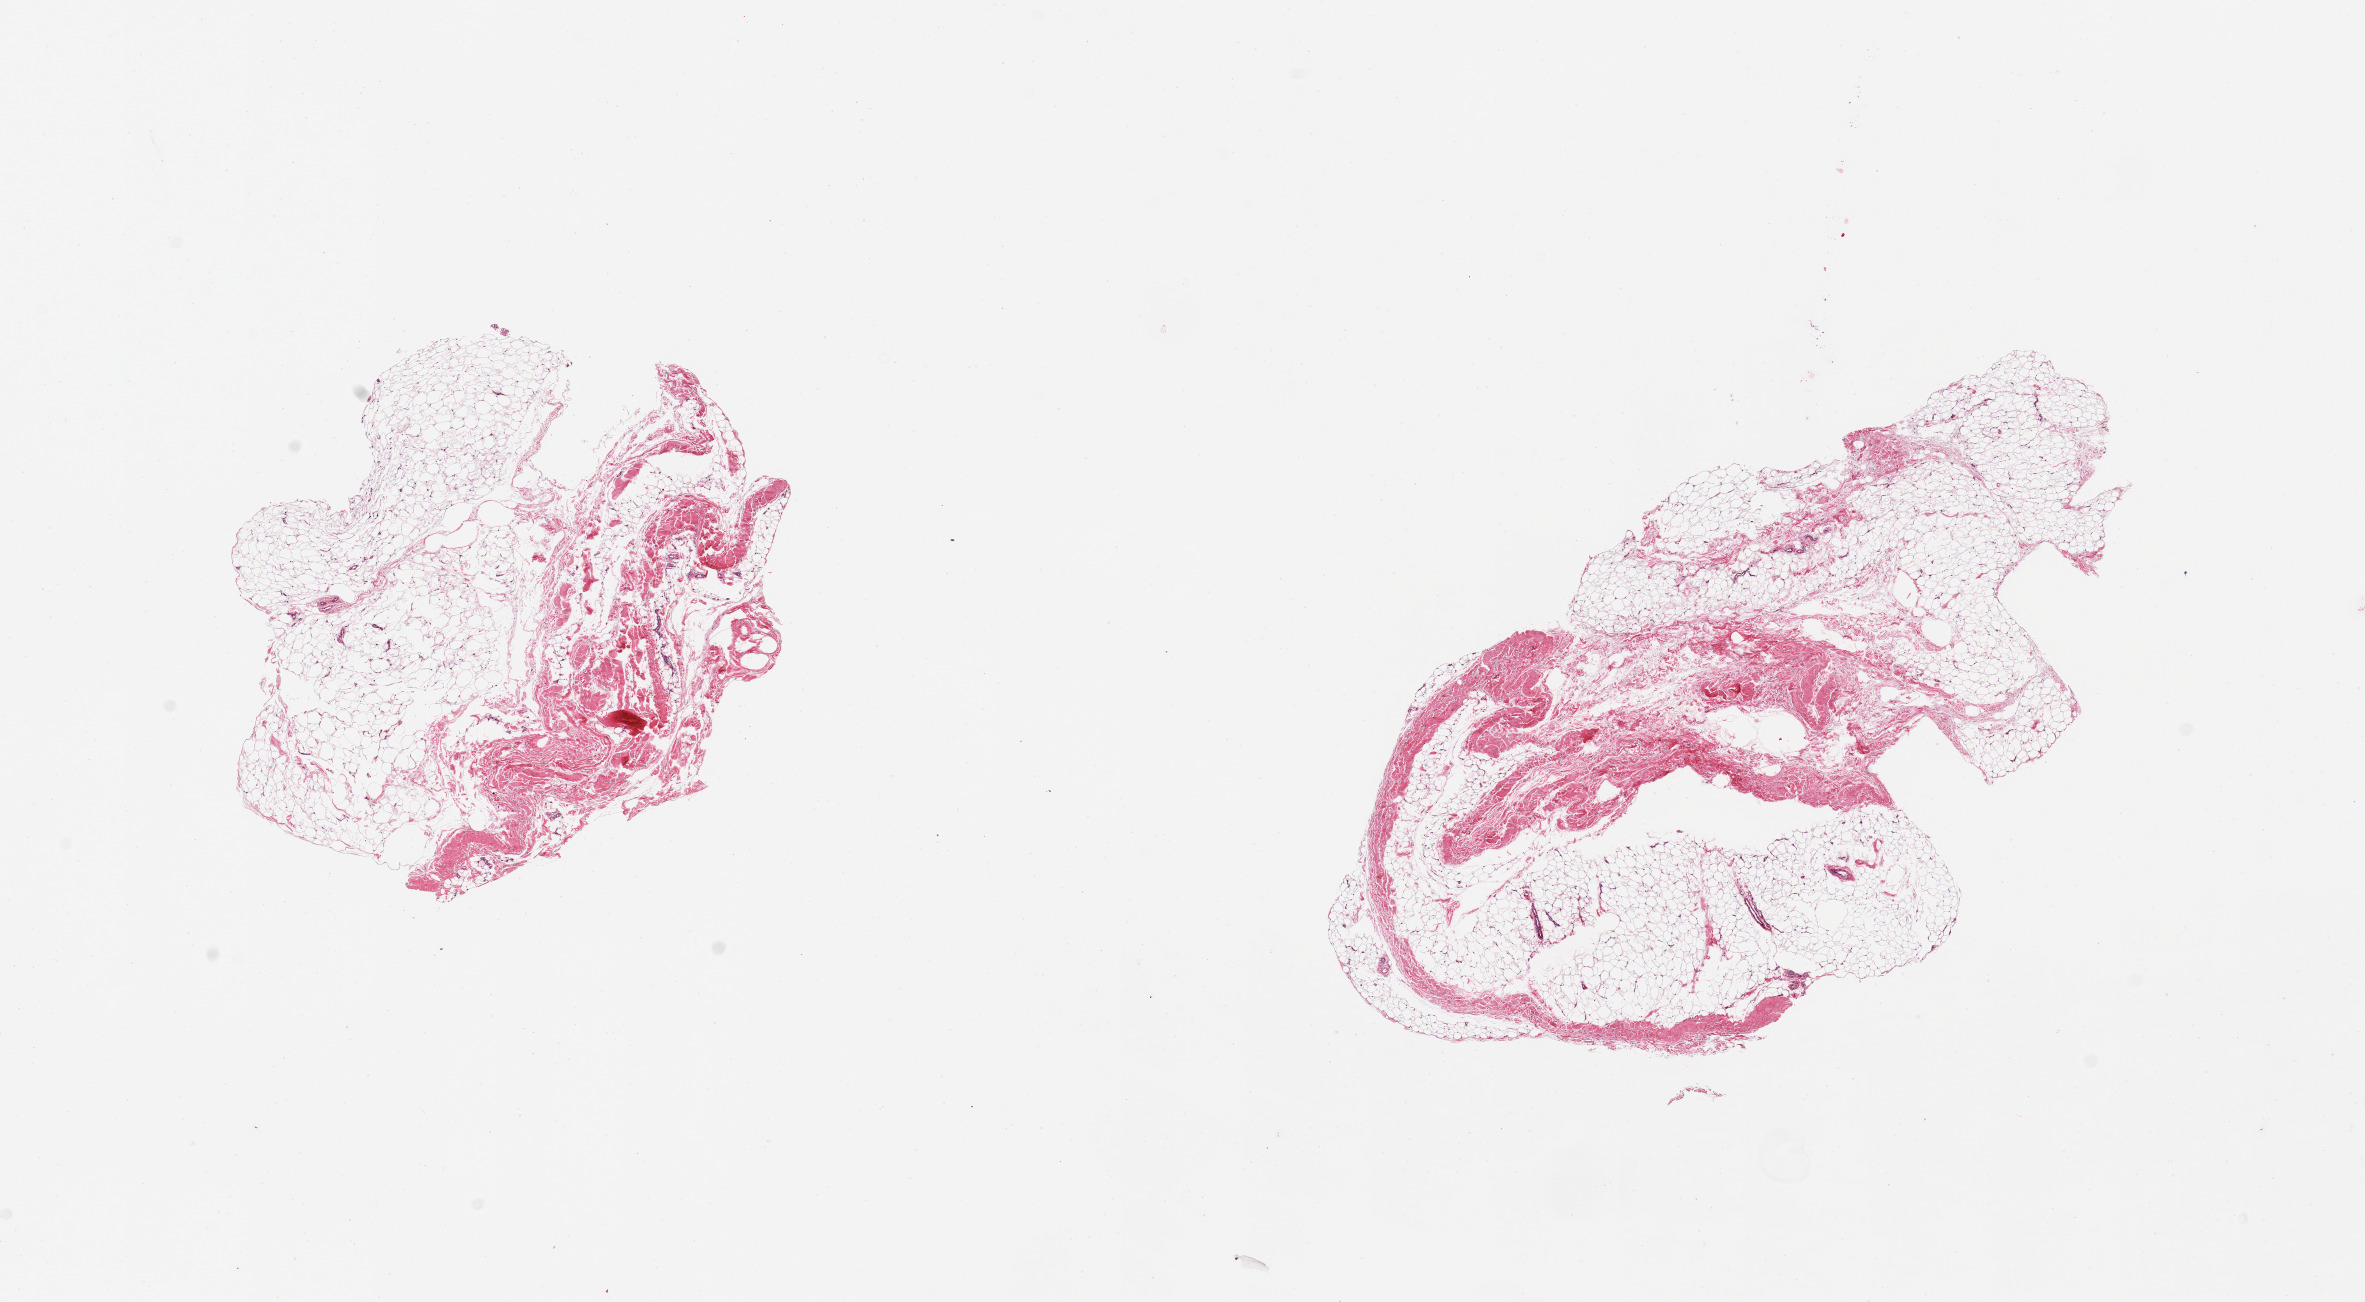
Hematoxylin and eosin (H&E) whole-slide image — a low-resolution overview of the entire scanned area, about 18.7 x 10.3 mm (acquisition: 20x scan). Female donor.
• specimen: PAXgene-fixed, paraffin-embedded tissue; sampled site (target tissue): tibial nerve; donor tissue sample